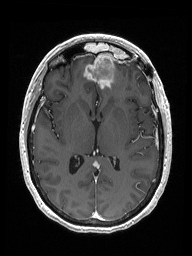
Brain MRI from a brain-tumour surgery series, one axial slice. T1-weighted post-contrast. 1 mm slice thickness. 192 × 256 image matrix. From the clinical record (not read from this slice): histopathology: Metastastic Carcinoma from Breast primary.
Outlined on this slice (expert manual segmentation):
- previous resection cavity: bounding box <86,53,115,80> (left, top, right, bottom; pixels)